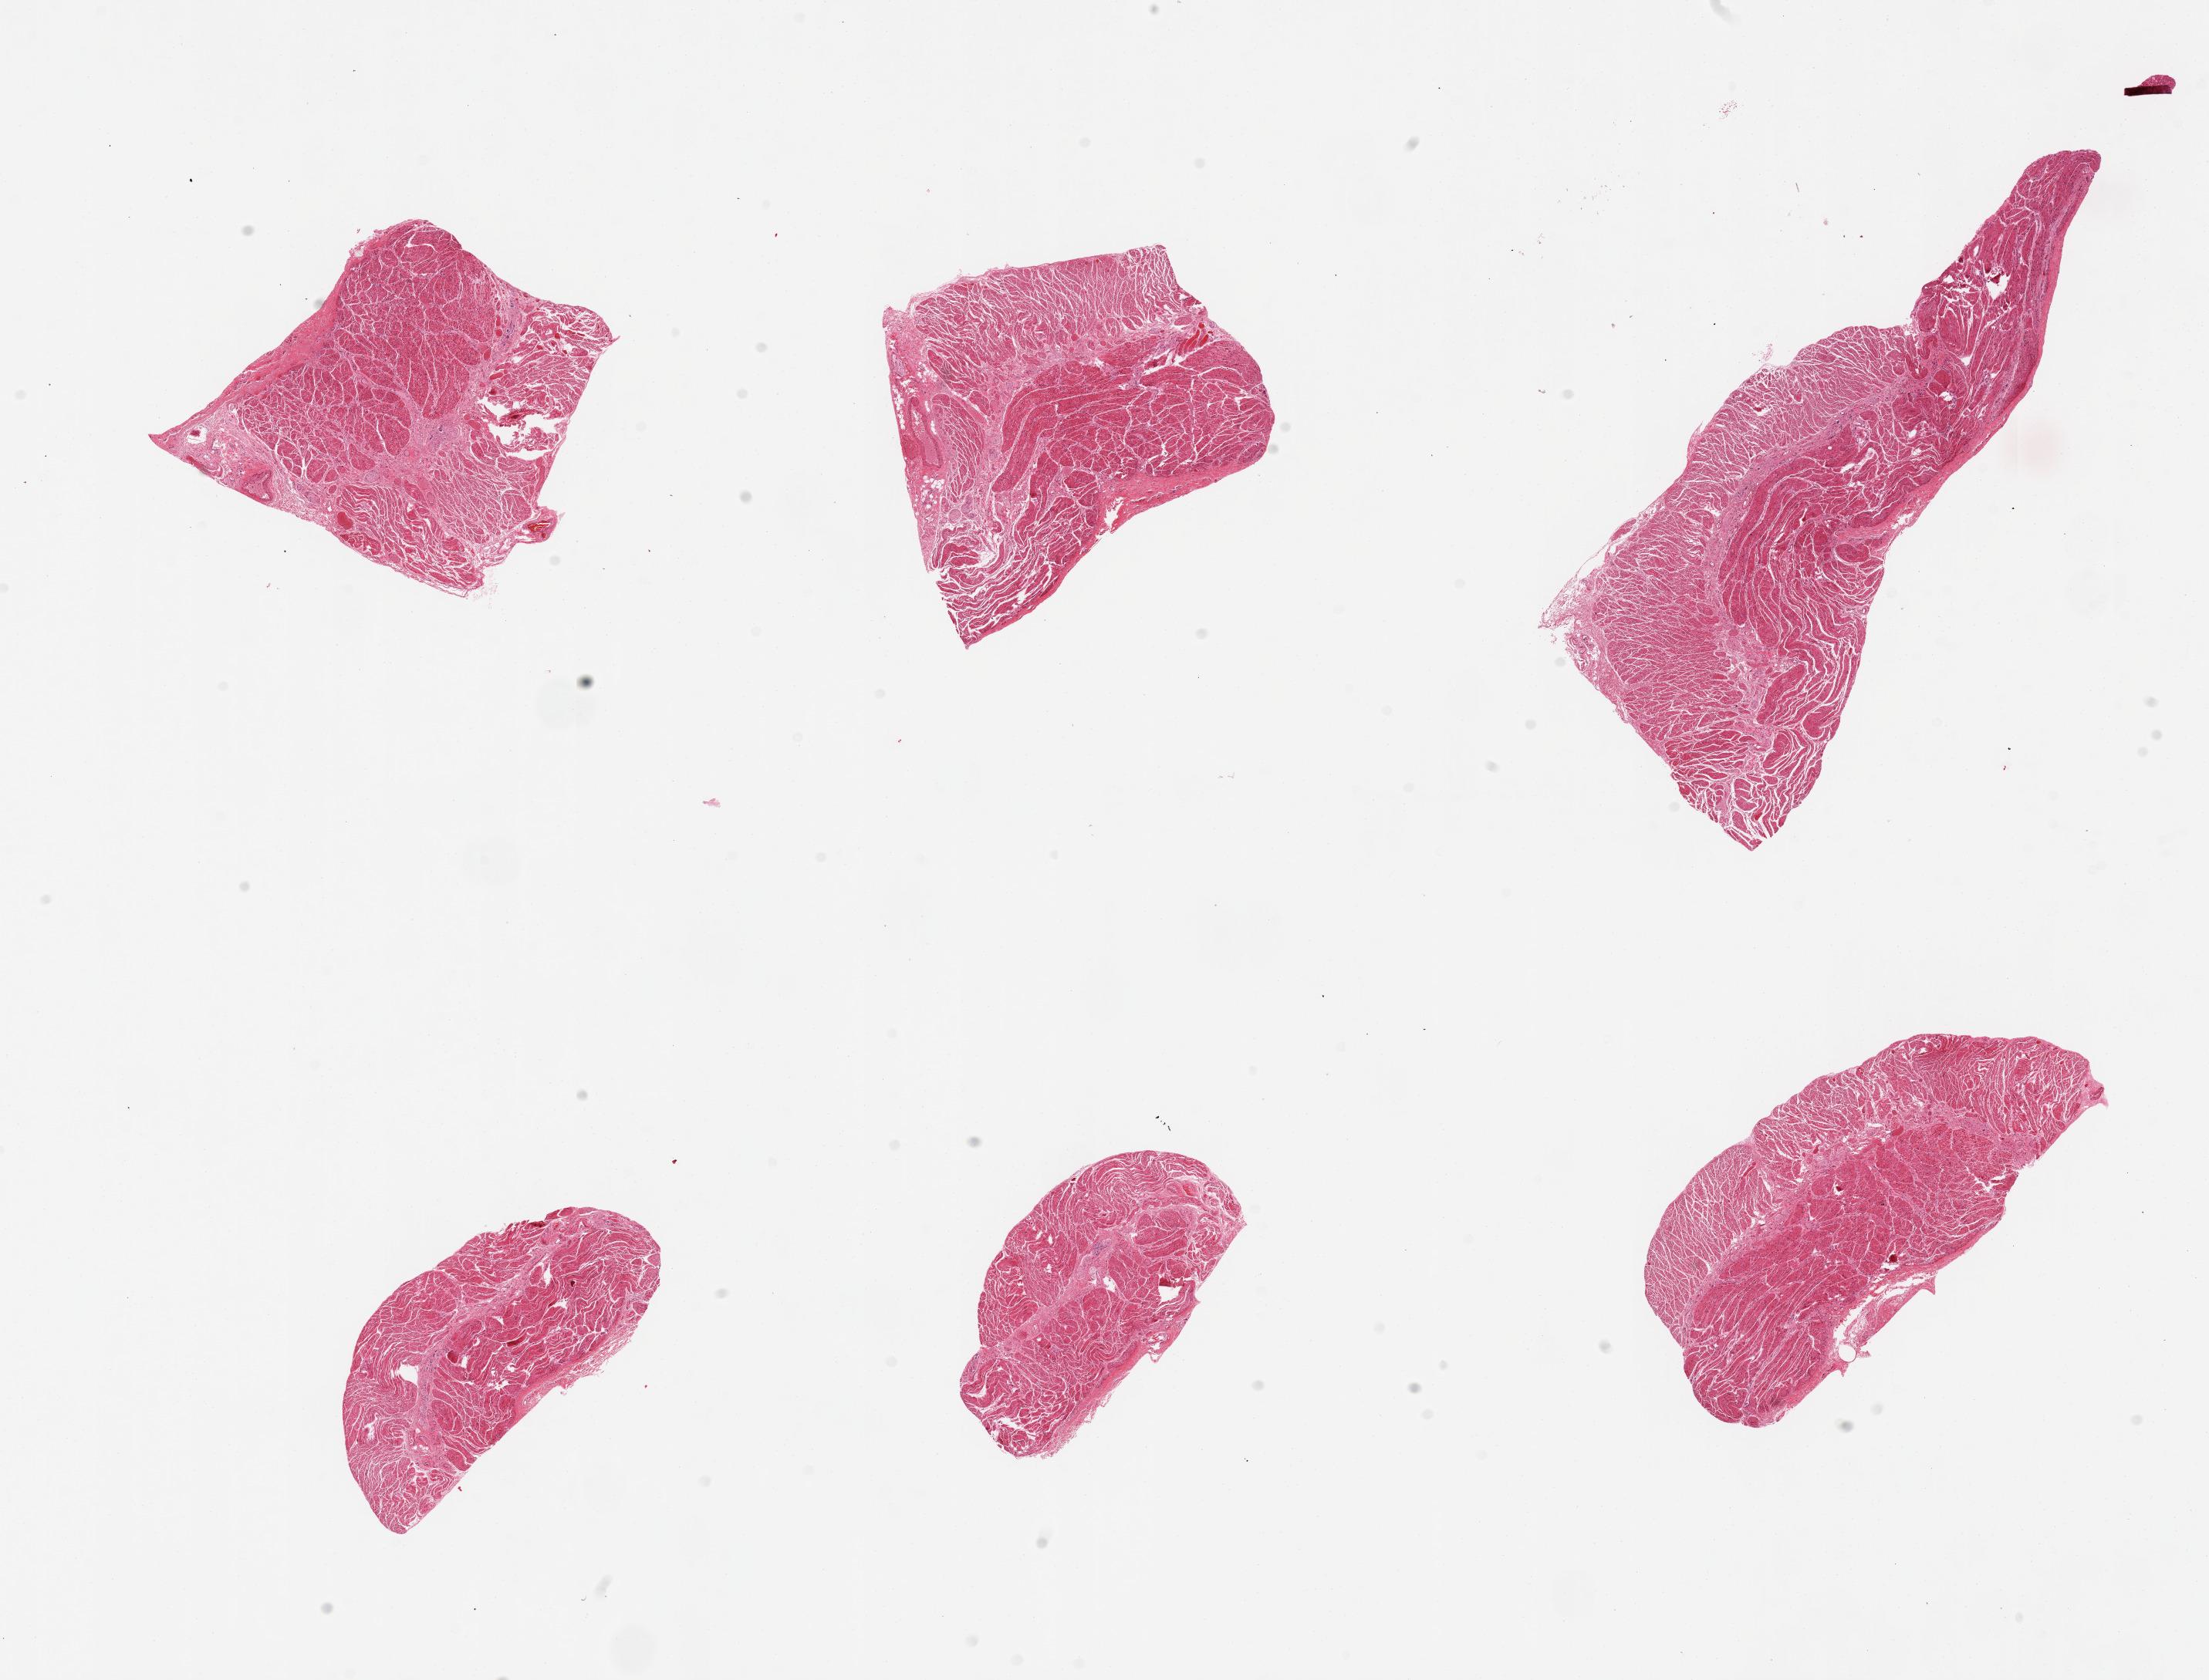
Haematoxylin and eosin whole-slide image, low-resolution overview of the scanned area, about 22.6 x 17.2 mm (acquisition: 20x scan). PAXgene-fixed paraffin-embedded (PFPE) section. Target tissue: esophageal muscle. Donor tissue sample. Donor sex: male.
• reviewer comment on this tissue sample: 6 pieces, well trimmed